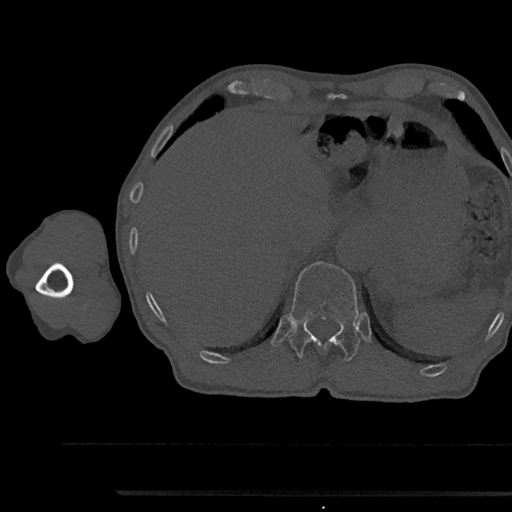
CT including the spine, one axial slice. Position 726 of 797 along the scan axis. Reconstruction kernel Br40s/3. Bone window (W 1800 / L 400 HU). 512 × 512 image matrix, field of view 367 × 367 mm. Male patient, age 79 years. From the clinical record (not read from this slice): primary cancer: prostate.
Annotated regions visible in this slice (semi-automatic segmentation, software-assisted and operator-edited):
- T12 vertebra: bounding box <289,261,361,360> (left, top, right, bottom; pixels)